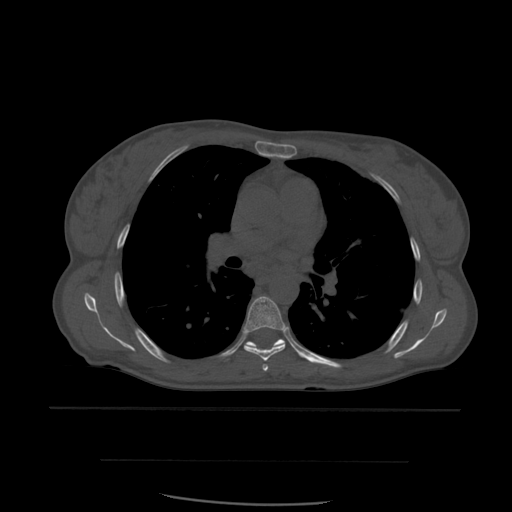
CT including the spine, one axial slice; position 388 of 574 along the scan axis; bone window (W 1800 / L 400 HU); 1.25 mm slice thickness; 512 × 512 image matrix, field of view 392 × 392 mm. Patient age 48 years. From the clinical record (not read from this slice): primary cancer: lung.
Outlined on this slice (semi-automatically segmented with operator editing):
- T5 vertebra: box from (x=262, y=364) to (x=269, y=372) px
- T6 vertebra: (x=244, y=297)–(x=289, y=361)
- T7 vertebra: (x=245, y=339)–(x=286, y=348)